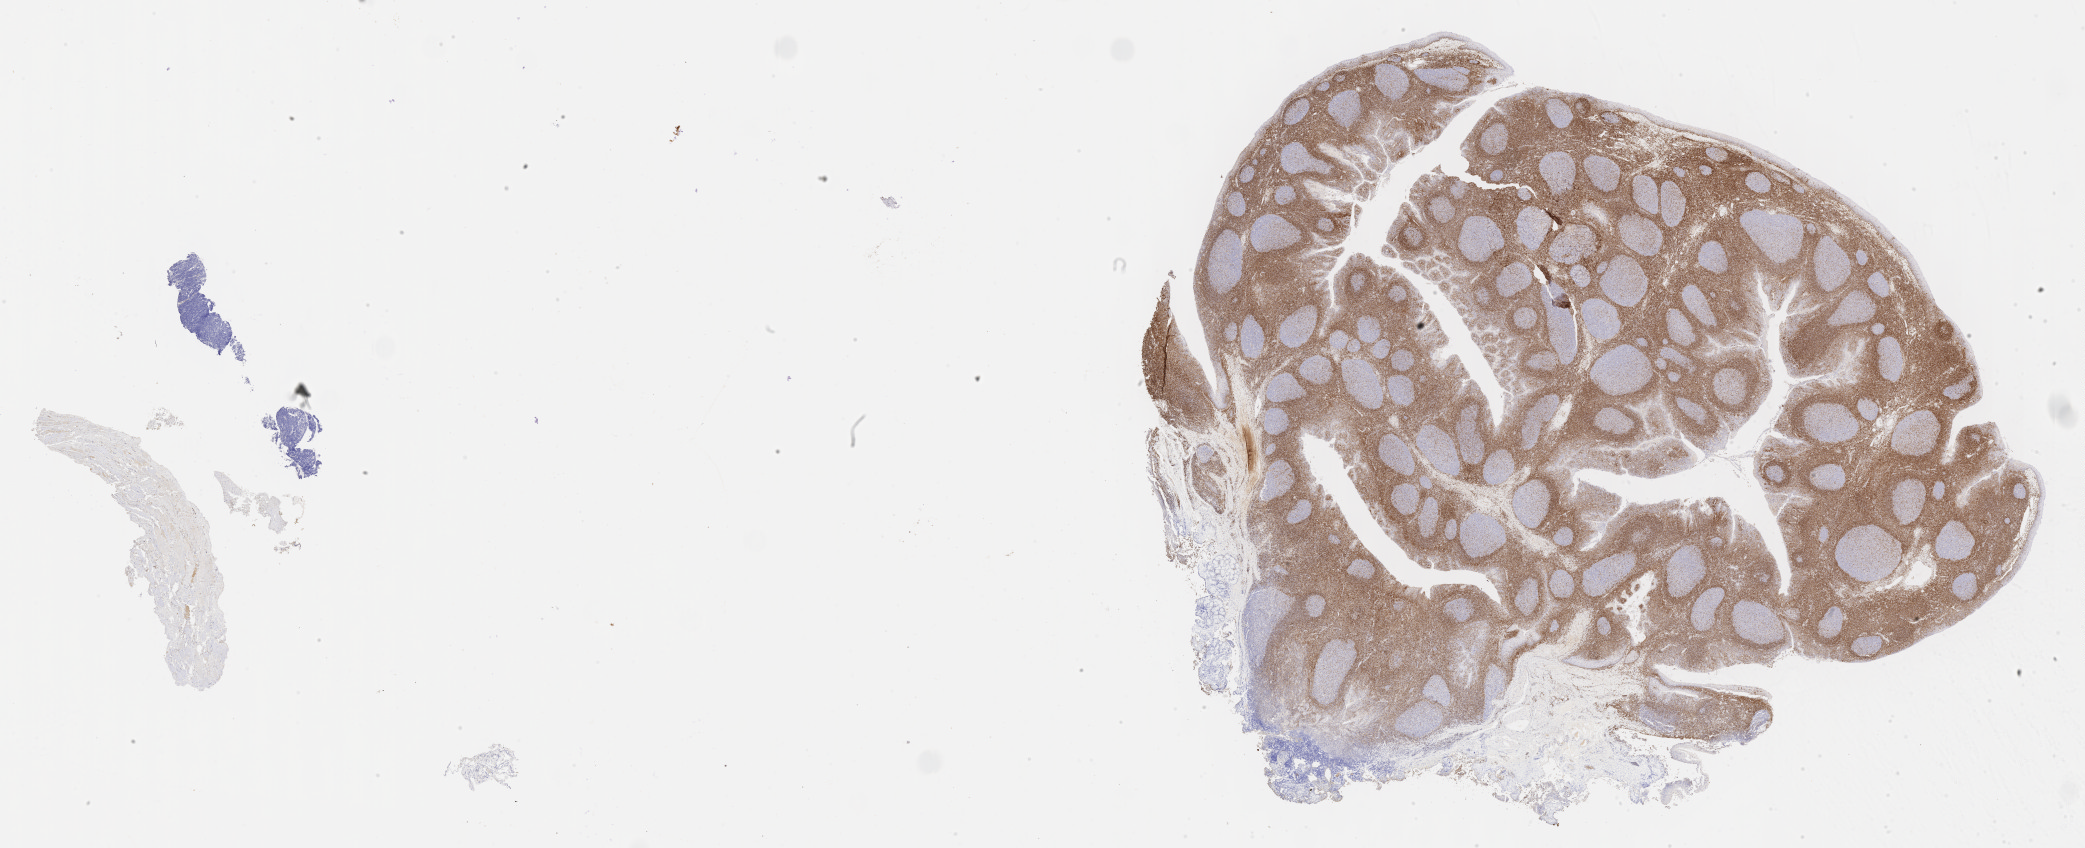
IHC for BCL2, whole-slide image — a low-resolution overview of the entire scanned area, about 33.7 x 13.7 mm, specimen: tumor tissue, anatomic site: liver. Patient sex: male.
* diagnosis: Burkitt lymphoma, NOS